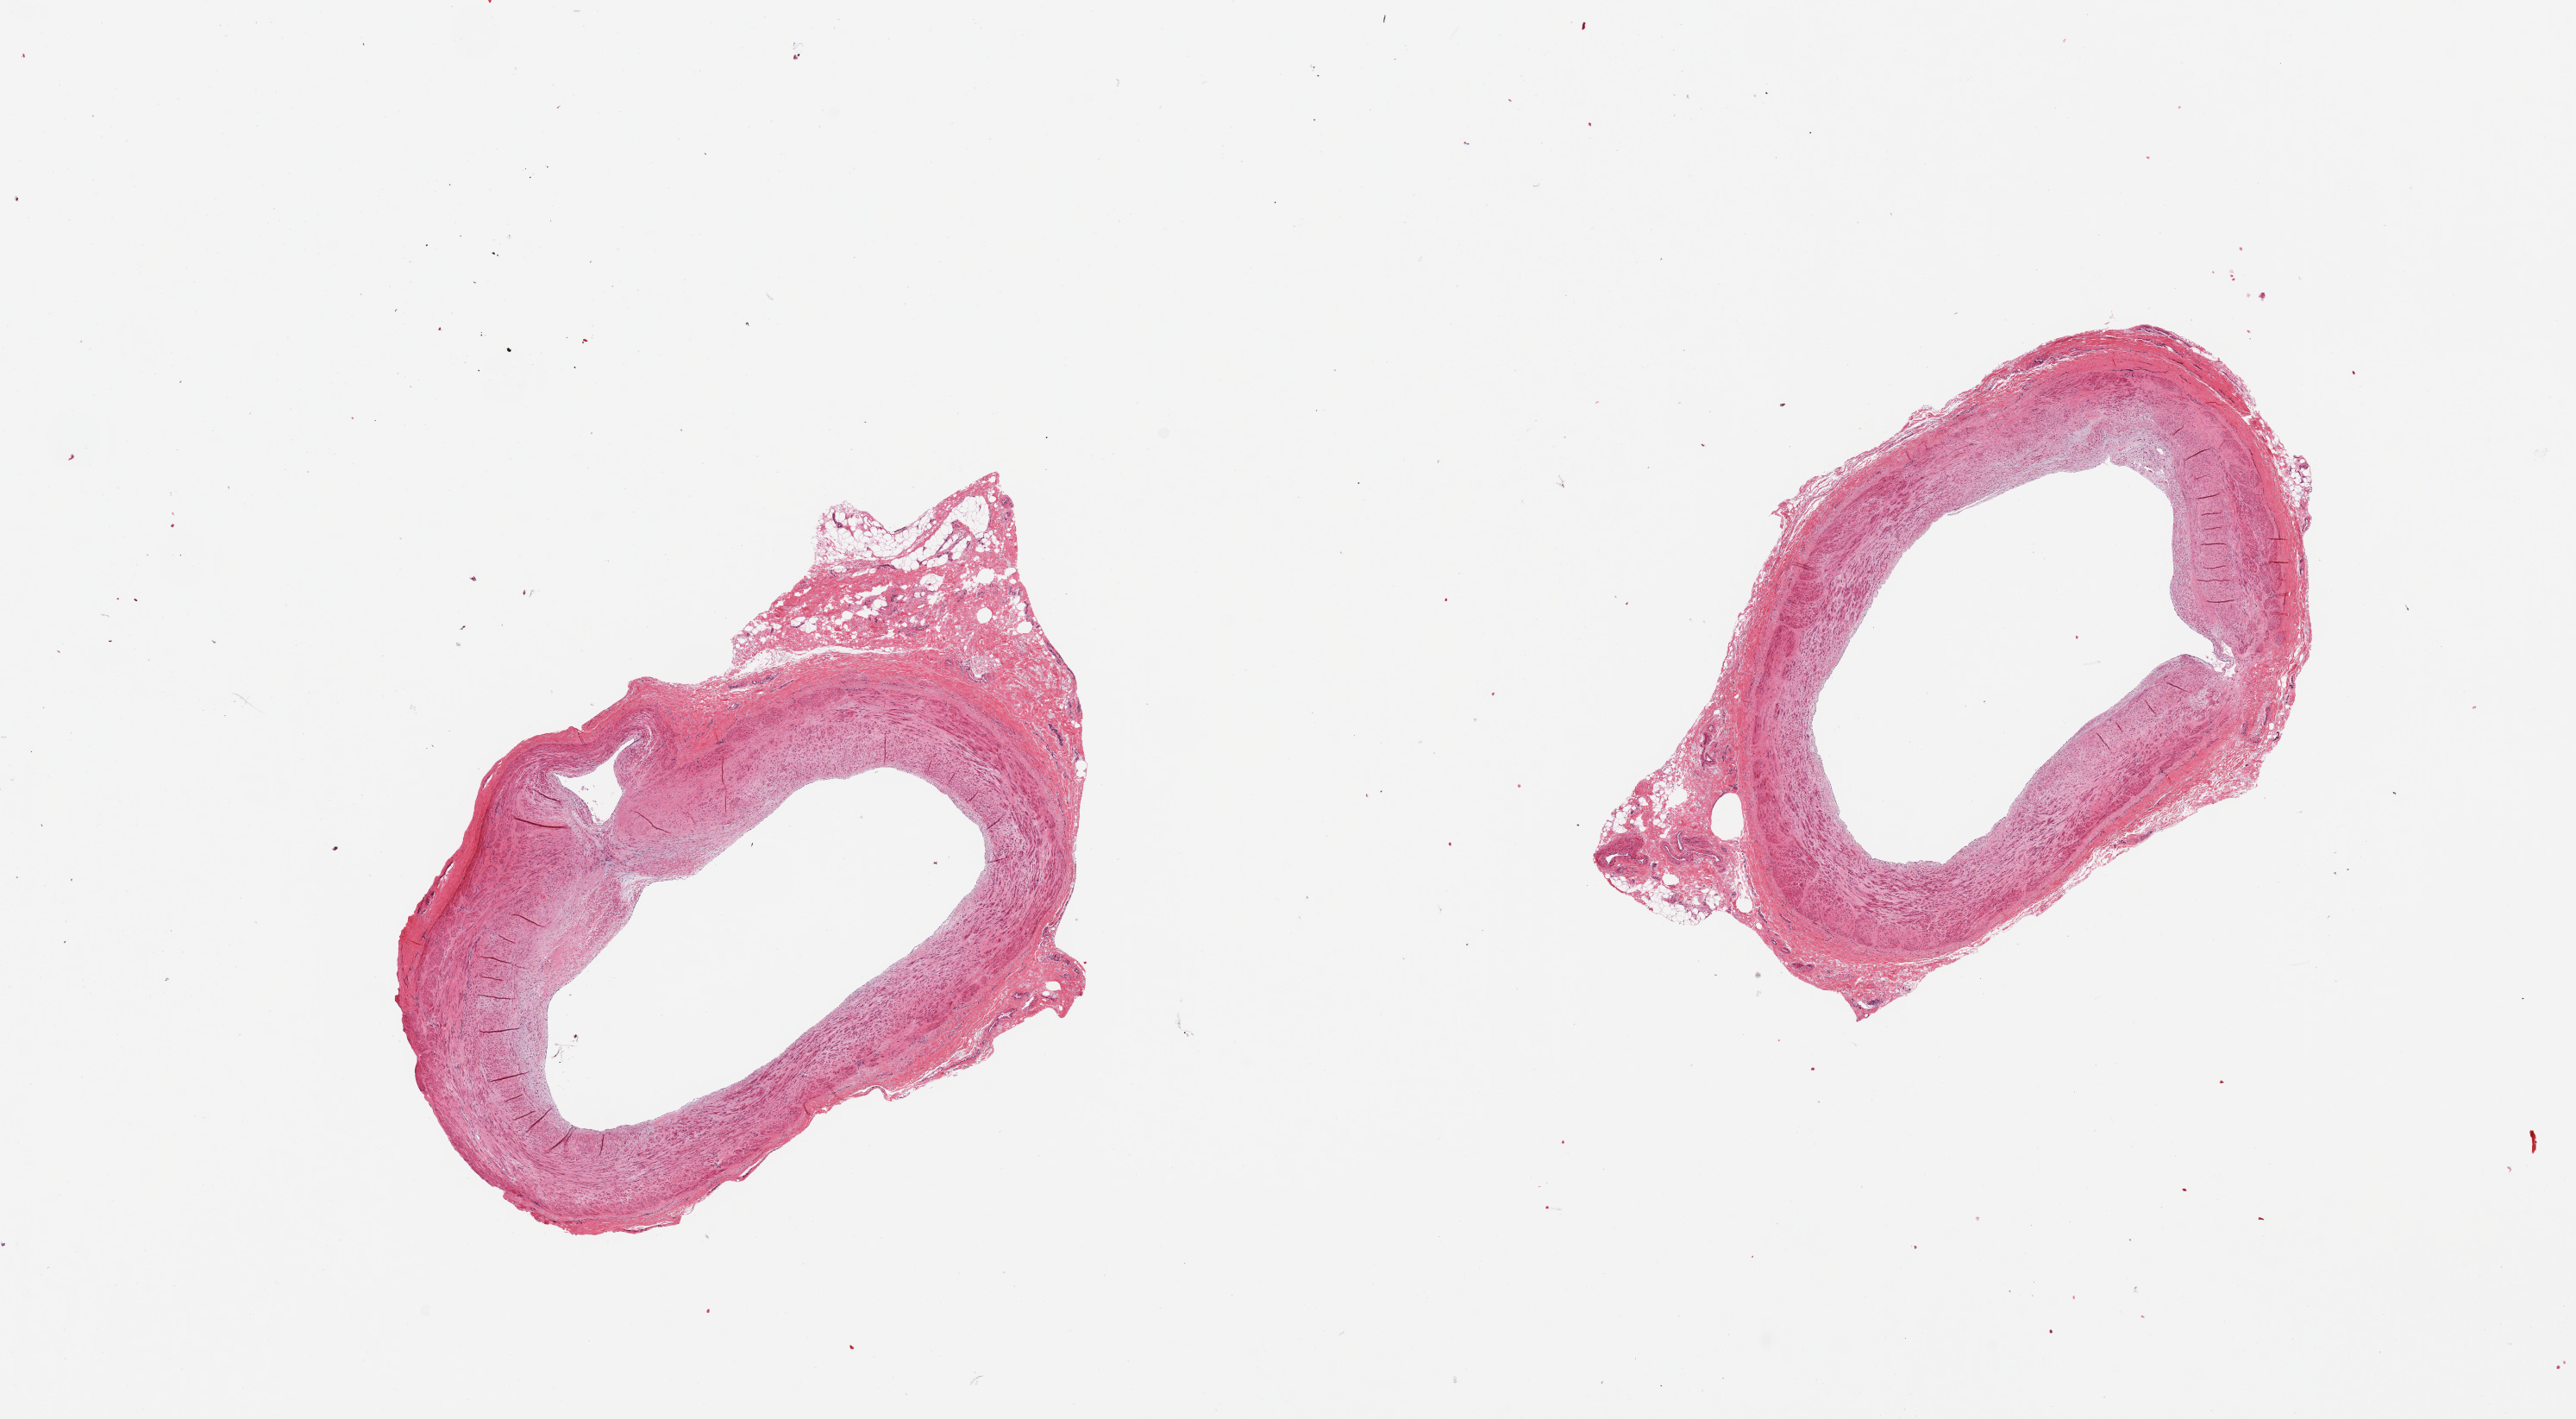
Digitized haematoxylin and eosin-stained section — low-resolution overview of the scanned area, about 23.6 x 13.0 mm. PAXgene-fixed, paraffin-embedded tissue. Section of tibial artery (target tissue). Tissue donor sample. Donor: male.
Pathologist's review note for this sample: 2 pieces. well trimmed.